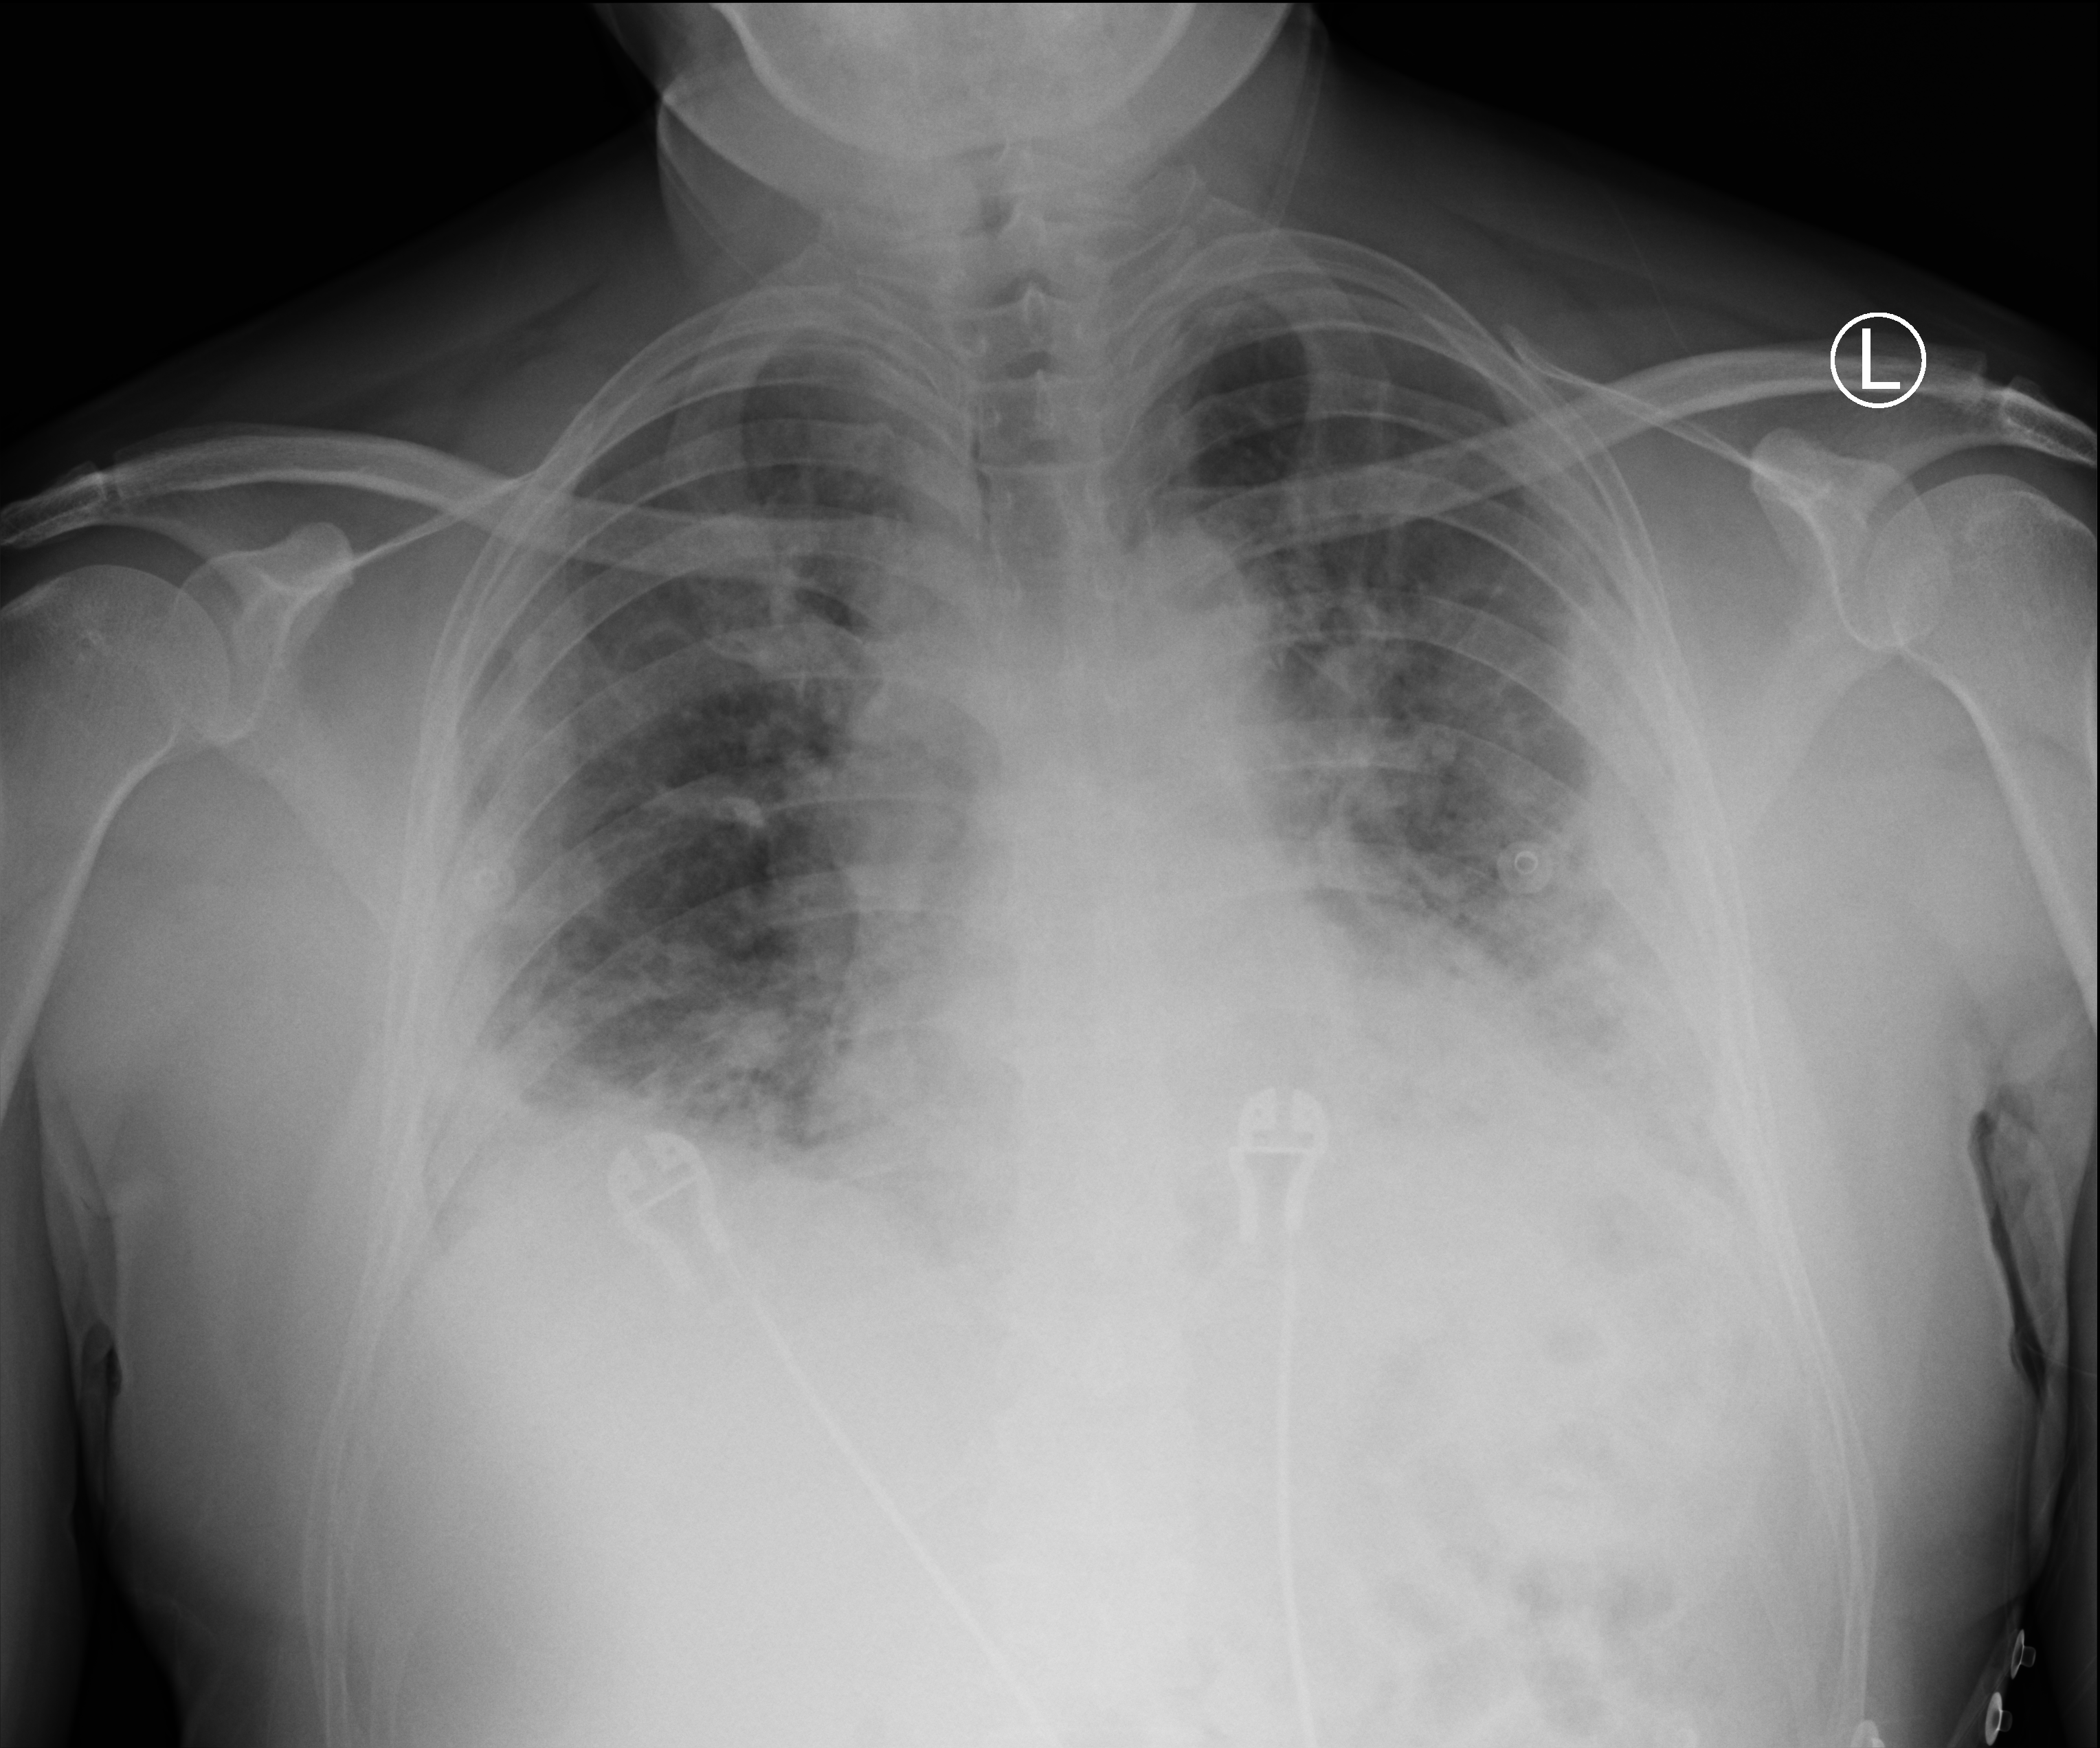
Chest X-ray (portable); anteroposterior (AP) projection. Male patient hospitalised with COVID-19, age 18–59 years.
Hospital-stay facts (about this admission, not read from this image; timing relative to this image not recorded): admitted to intensive care during this hospital stay: no; mechanically ventilated during this hospital stay: no.